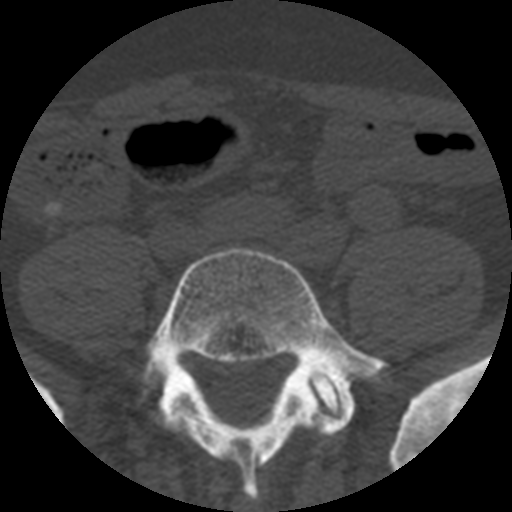
CT including the spine, one axial slice. Position 63 of 508 along the scan axis. Reconstruction kernel STANDARD. Bone window (W 1800 / L 400 HU). 512 × 512 image matrix, field of view 160 × 160 mm. Patient age 57 years. From the clinical record (not read from this slice): primary cancer: prostate.
Outlined on this slice (semi-automatic segmentation, software-assisted and operator-edited):
- L5 vertebra: bounding box <128,247,387,501> (left, top, right, bottom; pixels)